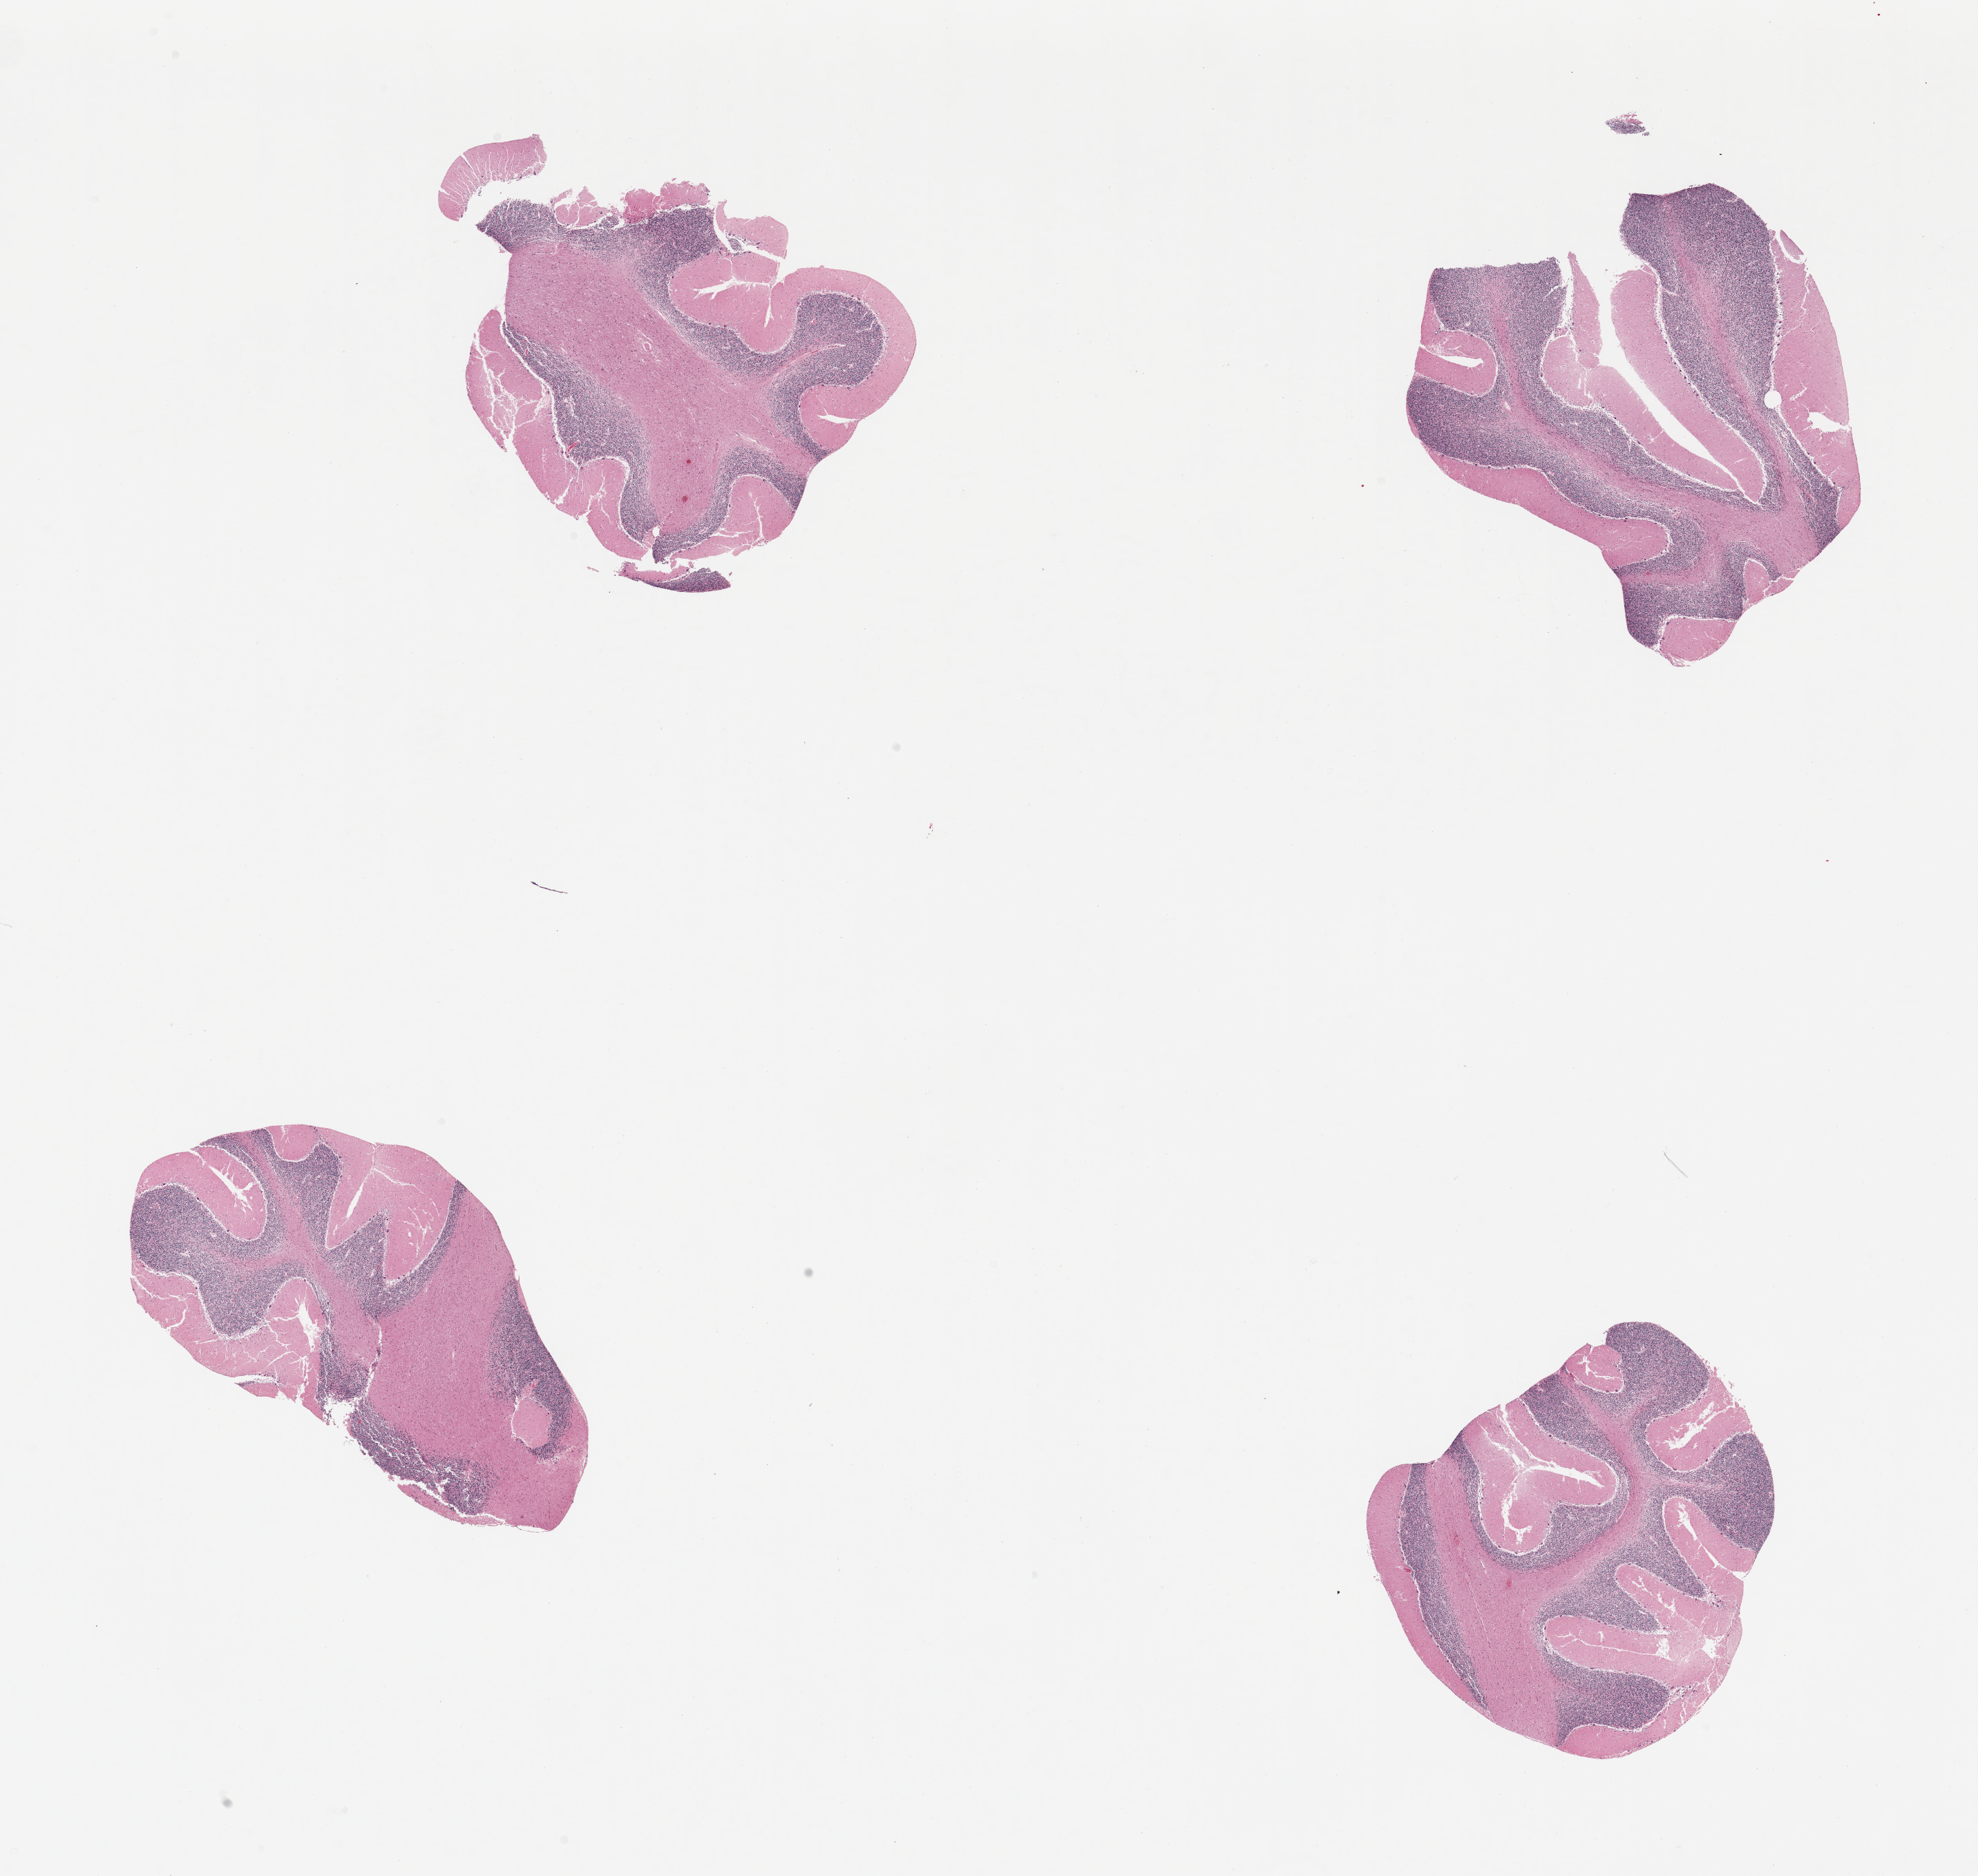
Whole-slide image, haematoxylin and eosin stain — whole scanned area (about 22.6 x 21.5 mm, slide scanned at 20x) shown as a low-resolution overview. PAXgene-fixed, paraffin-embedded tissue. Sampled site (target tissue): cerebellum. Donor tissue sample. Male donor.
Reviewer comment on this tissue sample: 4 pieces.